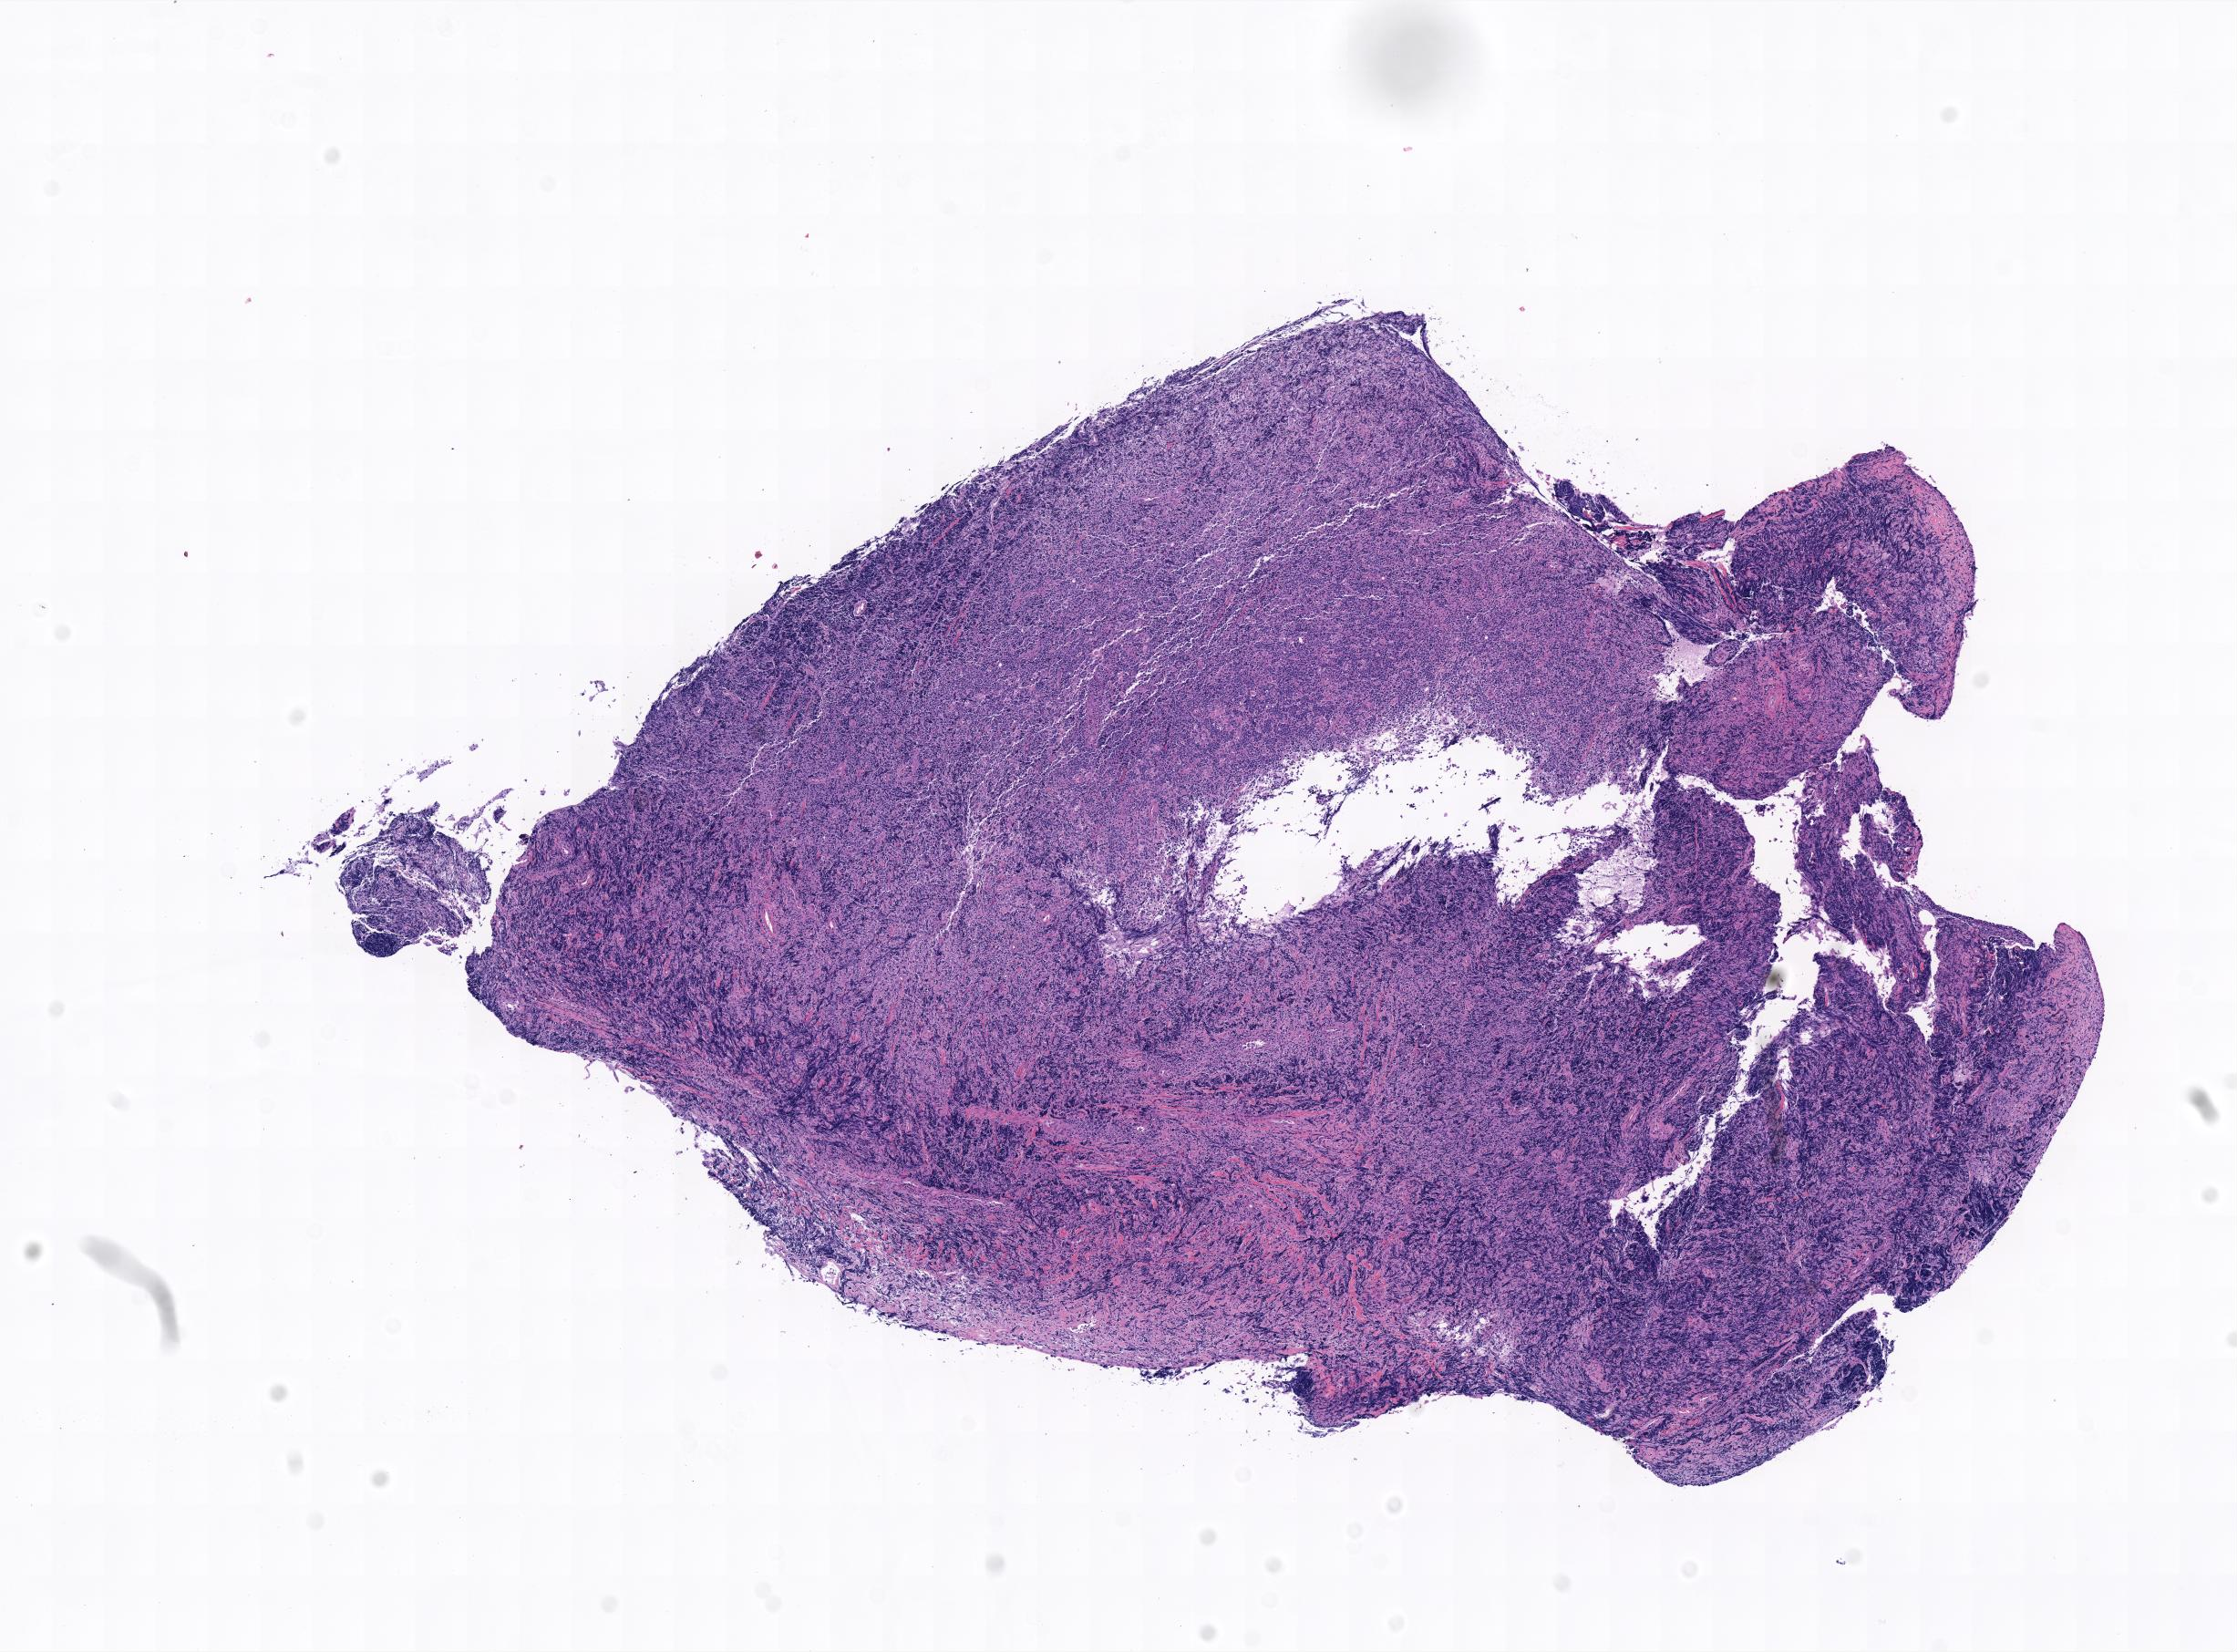
Digitized haematoxylin and eosin-stained section — whole scanned area shown as a low-resolution overview, tumor tissue, site: ovary. Female, age 3 years at initial diagnosis.
• histologic diagnosis: Burkitt lymphoma, NOS